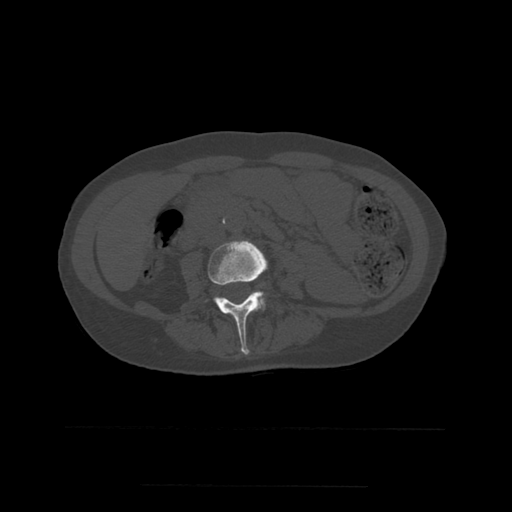
CT including the spine, one axial slice. Slice 185 of 544 in the series (ordered by position). Bone window (W 1800 / L 400 HU). 1.25 mm slice thickness. 512 × 512 image matrix, field of view 350 × 350 mm. Patient age 58 years. From the clinical record (not read from this slice): primary cancer: lung.
Outlined on this slice (semi-automatic segmentation, software-assisted and operator-edited):
- L3 vertebra: bounding box (x1, y1, x2, y2) in pixels: (205, 241, 267, 355)
- L4 vertebra: (255, 291, 265, 309)